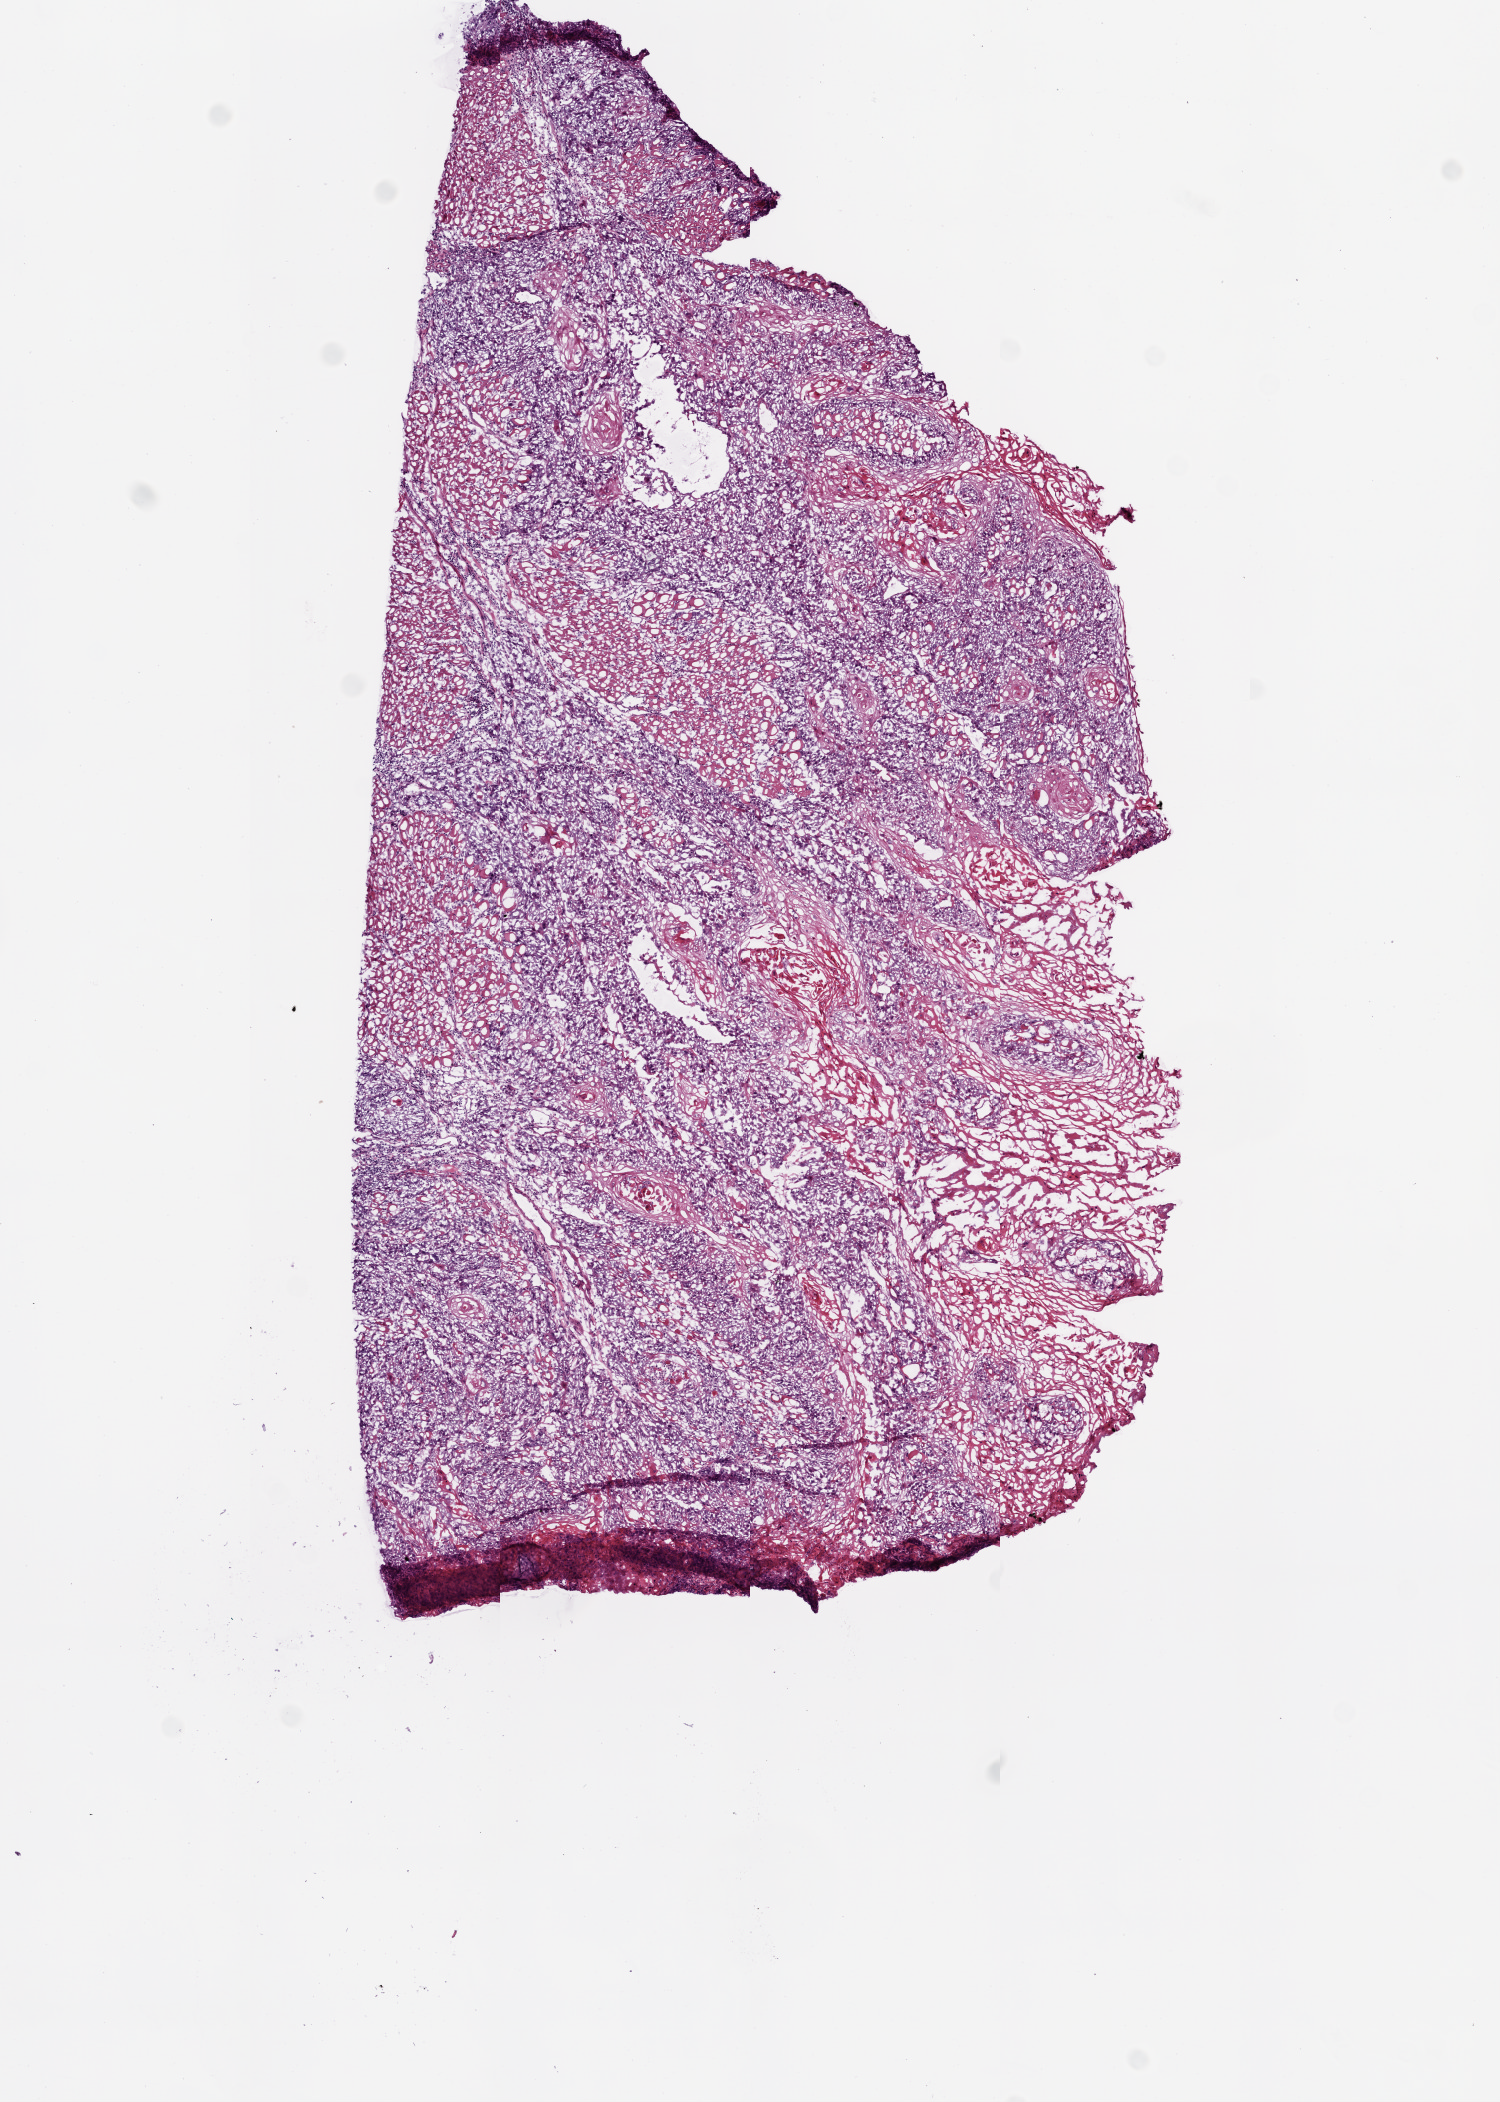
H&E-stained whole-slide image, shown as a low-resolution overview of the whole scanned area (about 6.0 x 8.4 mm, slide scanned at 20x). Frozen section from the top of the tissue portion. Primary tumour sample from the head and neck. Male patient; age at initial diagnosis 60 years. Histologic grade: G2 (moderately differentiated). Composition of this section per pathologist review: tumour cells 85%, tumour nuclei 85%, normal cells 0%, stromal cells 15%, necrosis 0%.
AJCC pathologic stage: II (7th edition). Histologic diagnosis: Squamous cell carcinoma, NOS (tongue, NOS). TNM: T2 N0.